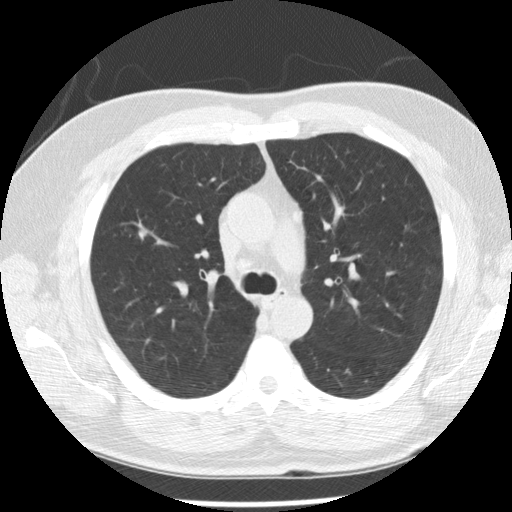
Low-dose screening chest CT, axial slice. Baseline annual screen. Lung window (W 1500 / L -600 HU). 2.5 mm slice thickness. Standard (soft-tissue) reconstruction kernel (STANDARD). 120 kVp. Slice 87 of 265 in the series. Male, age 57 years at enrolment.
• Lesion marked by an expert reader, bounding box <126,221,159,253> (left, top, right, bottom; pixels).
• Reader record for this screening exam (exam-level; its link to the box is not recorded): non-calcified nodule or mass ≥4 mm, right upper lobe, 7 × 7 mm, poorly defined margins, soft tissue attenuation.
• Participant outcome: lung cancer diagnosed 125 days after this screen — squamous cell carcinoma, NOS, right upper lobe, moderately differentiated (G2), stage IA (AJCC 6th edition), 10 mm at pathology.